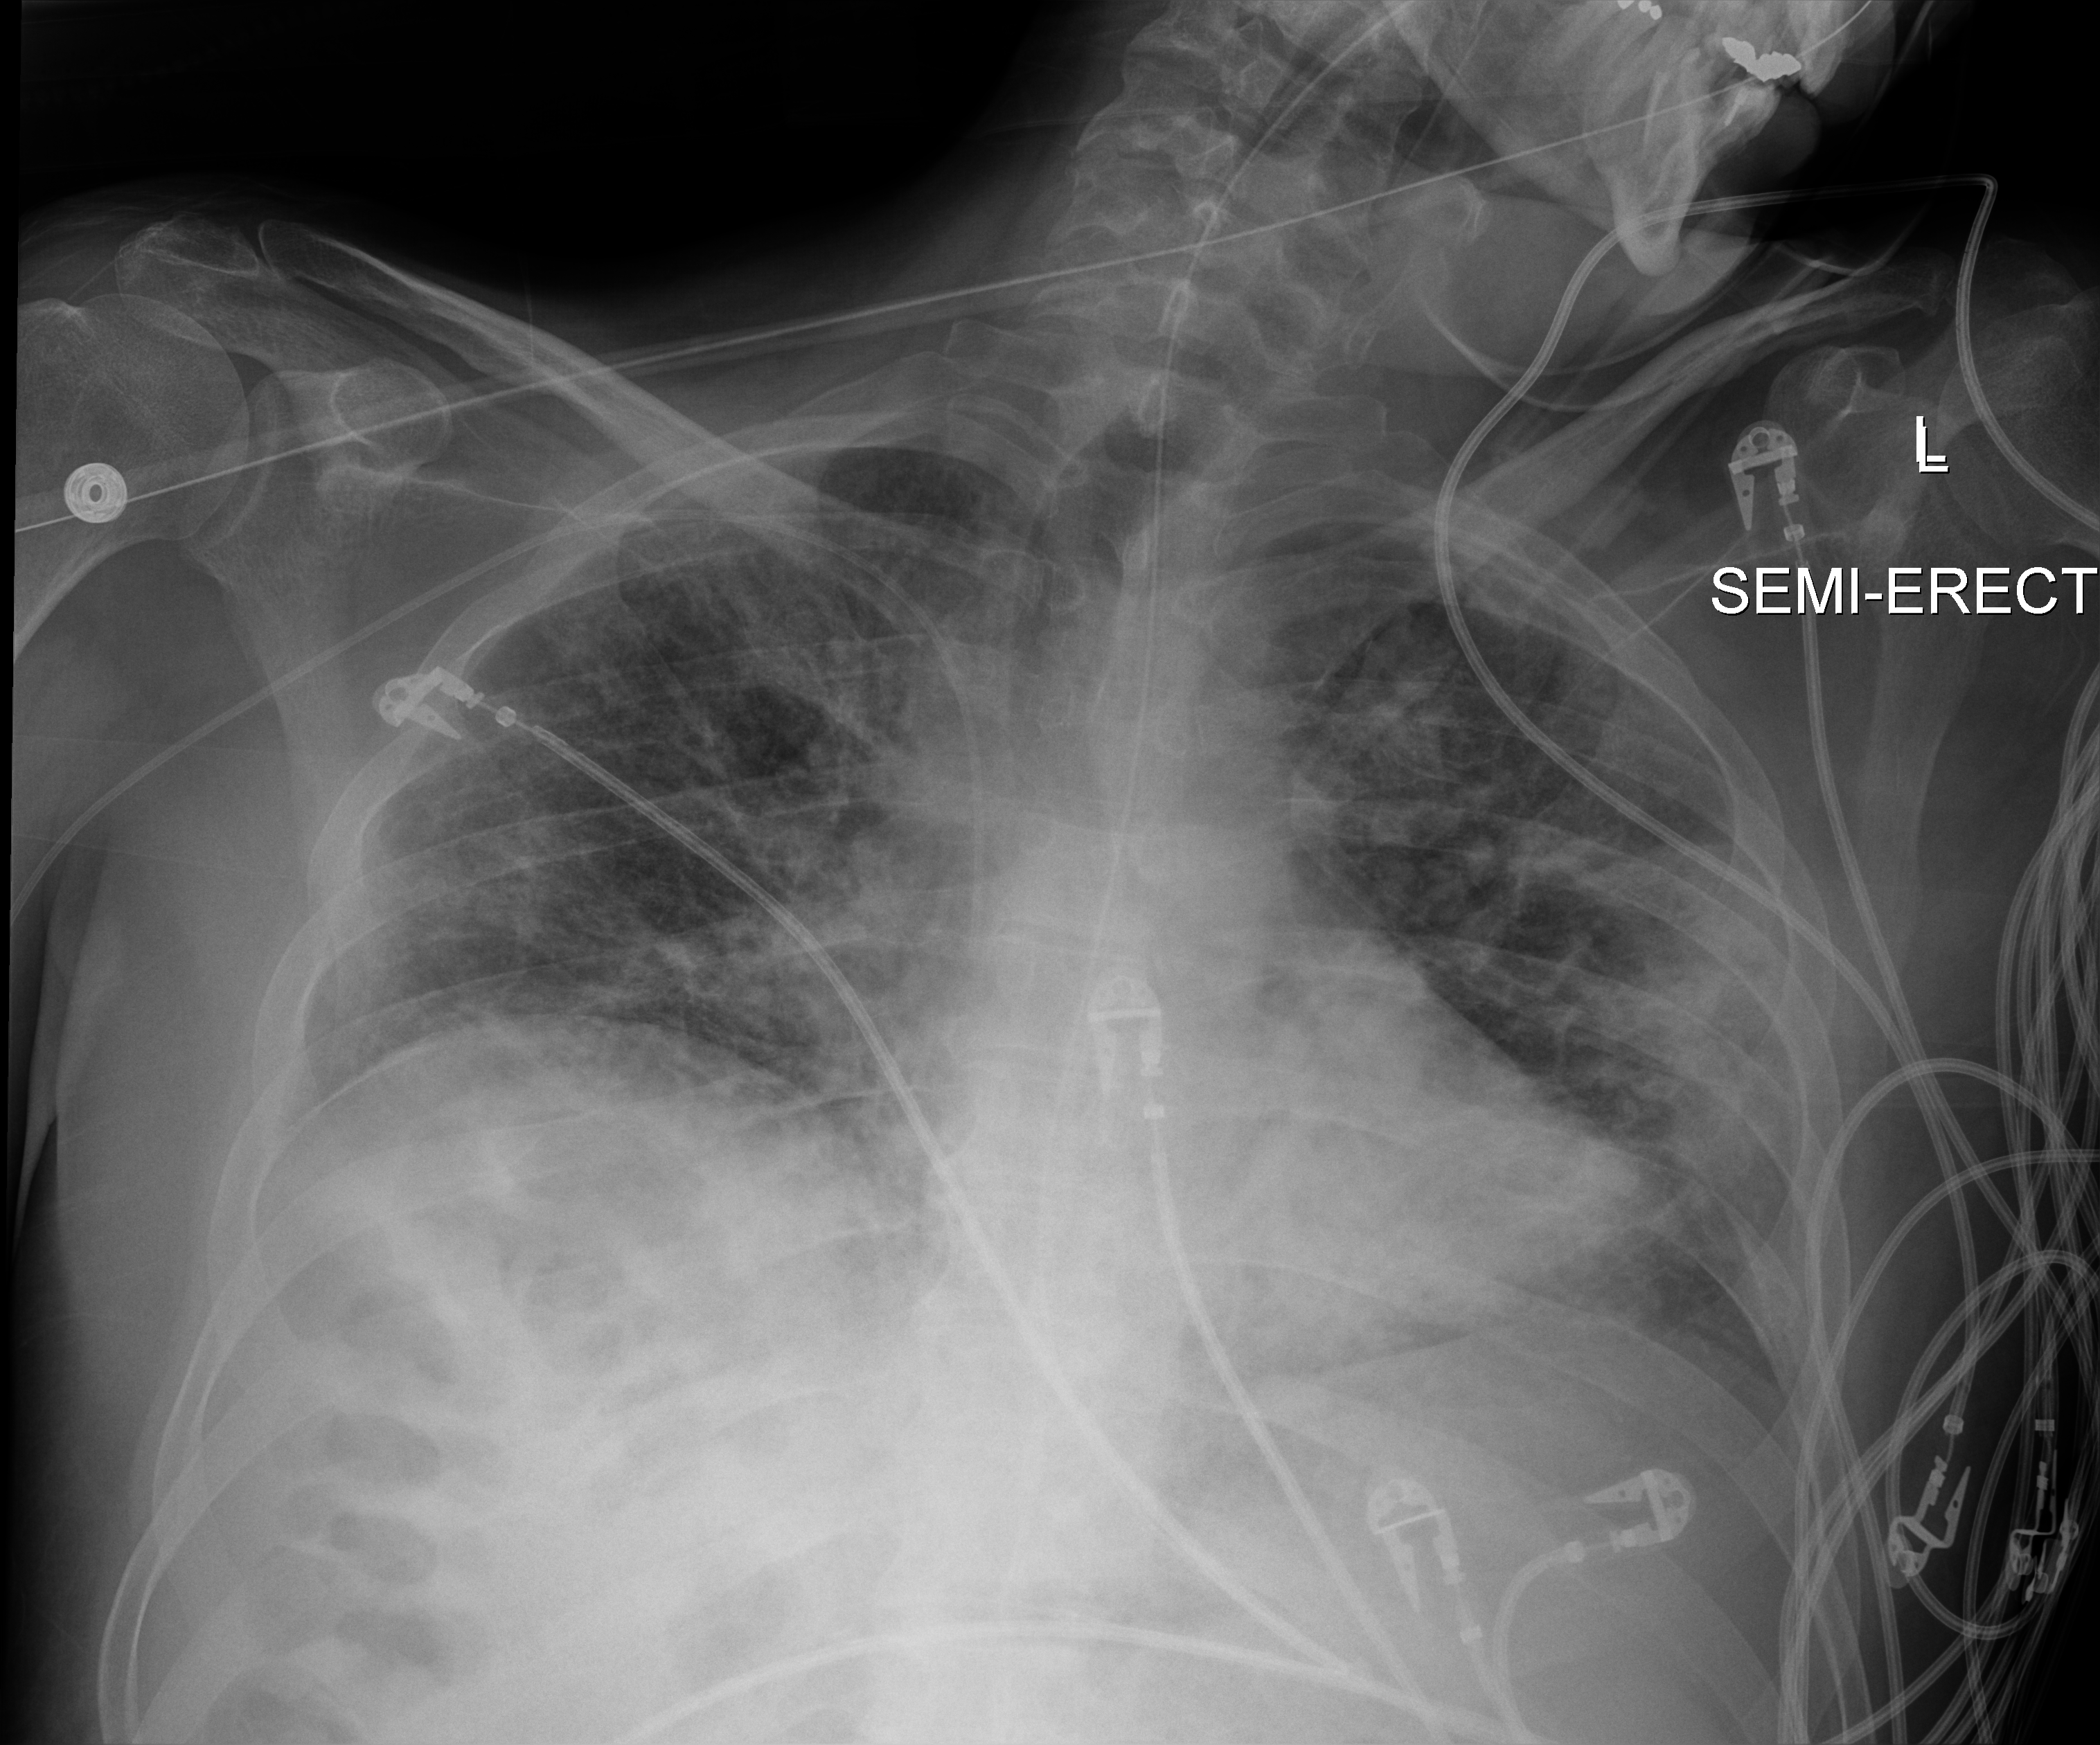
Chest X-ray (portable); anteroposterior (AP) projection. Patient hospitalised with COVID-19; male, aged 18–59 years.
Hospital-stay facts (about this admission, not read from this image; timing relative to this image not recorded): admitted to intensive care during this hospital stay: yes; diabetes (admission record): no; COPD (admission record): no.